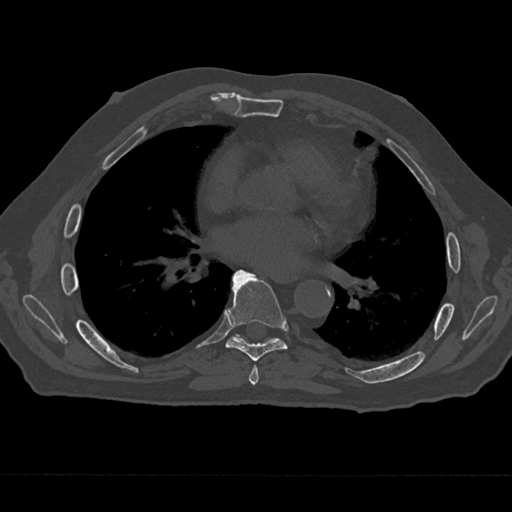
CT including the spine, one axial slice; slice 364 of 797 in the series (ordered by position); bone window (W 1800 / L 400 HU); 0.5 mm slice thickness; 512 × 512 image matrix. Patient: male, 75 years. Case-level facts recorded for this patient, not image findings: primary cancer: renal.
Outlined on this slice (semi-automatic segmentation, software-assisted and operator-edited):
- T6 vertebra: bounding box [x1, y1, x2, y2] px = [249, 365, 259, 385]
- T7 vertebra: [226, 270, 287, 361]
- T8 vertebra: [236, 335, 273, 340]